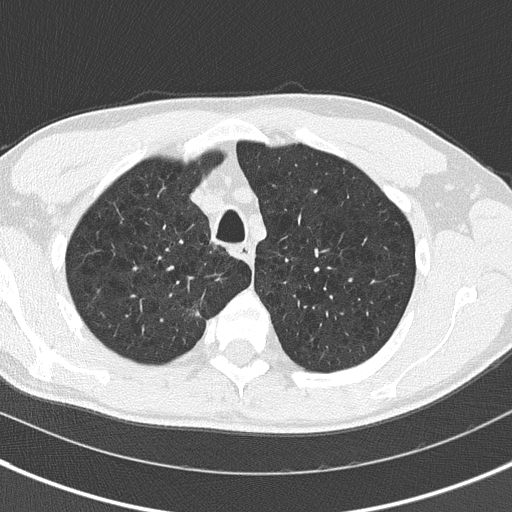
Low-dose screening chest CT, axial slice; first (baseline) screen; lung window (W 1500 / L -600 HU); 2 mm slice thickness; lung (sharp) reconstruction kernel (B50f); 120 kVp; 512 × 512 image matrix. Male participant, aged 56 years at enrolment. Current smoker at enrolment.
Lesion marked by an expert reader, bounding box <179,294,220,339> (left, top, right, bottom; pixels). The screening reader recorded 3 non-calcified nodules or masses ≥4 mm on this exam (right upper lobe, right upper lobe, left lower lobe); which of them this box marks is not recorded. Official screen result: positive, change unspecified: nodule(s) >= 4 mm or enlarging nodule(s), mass(es), or other non-specific abnormalities suspicious for lung cancer. Participant outcome: lung cancer diagnosed 228 days after this screen — non-small cell carcinoma, right upper lobe, stage IIIA (AJCC 6th edition), 21 mm at pathology.